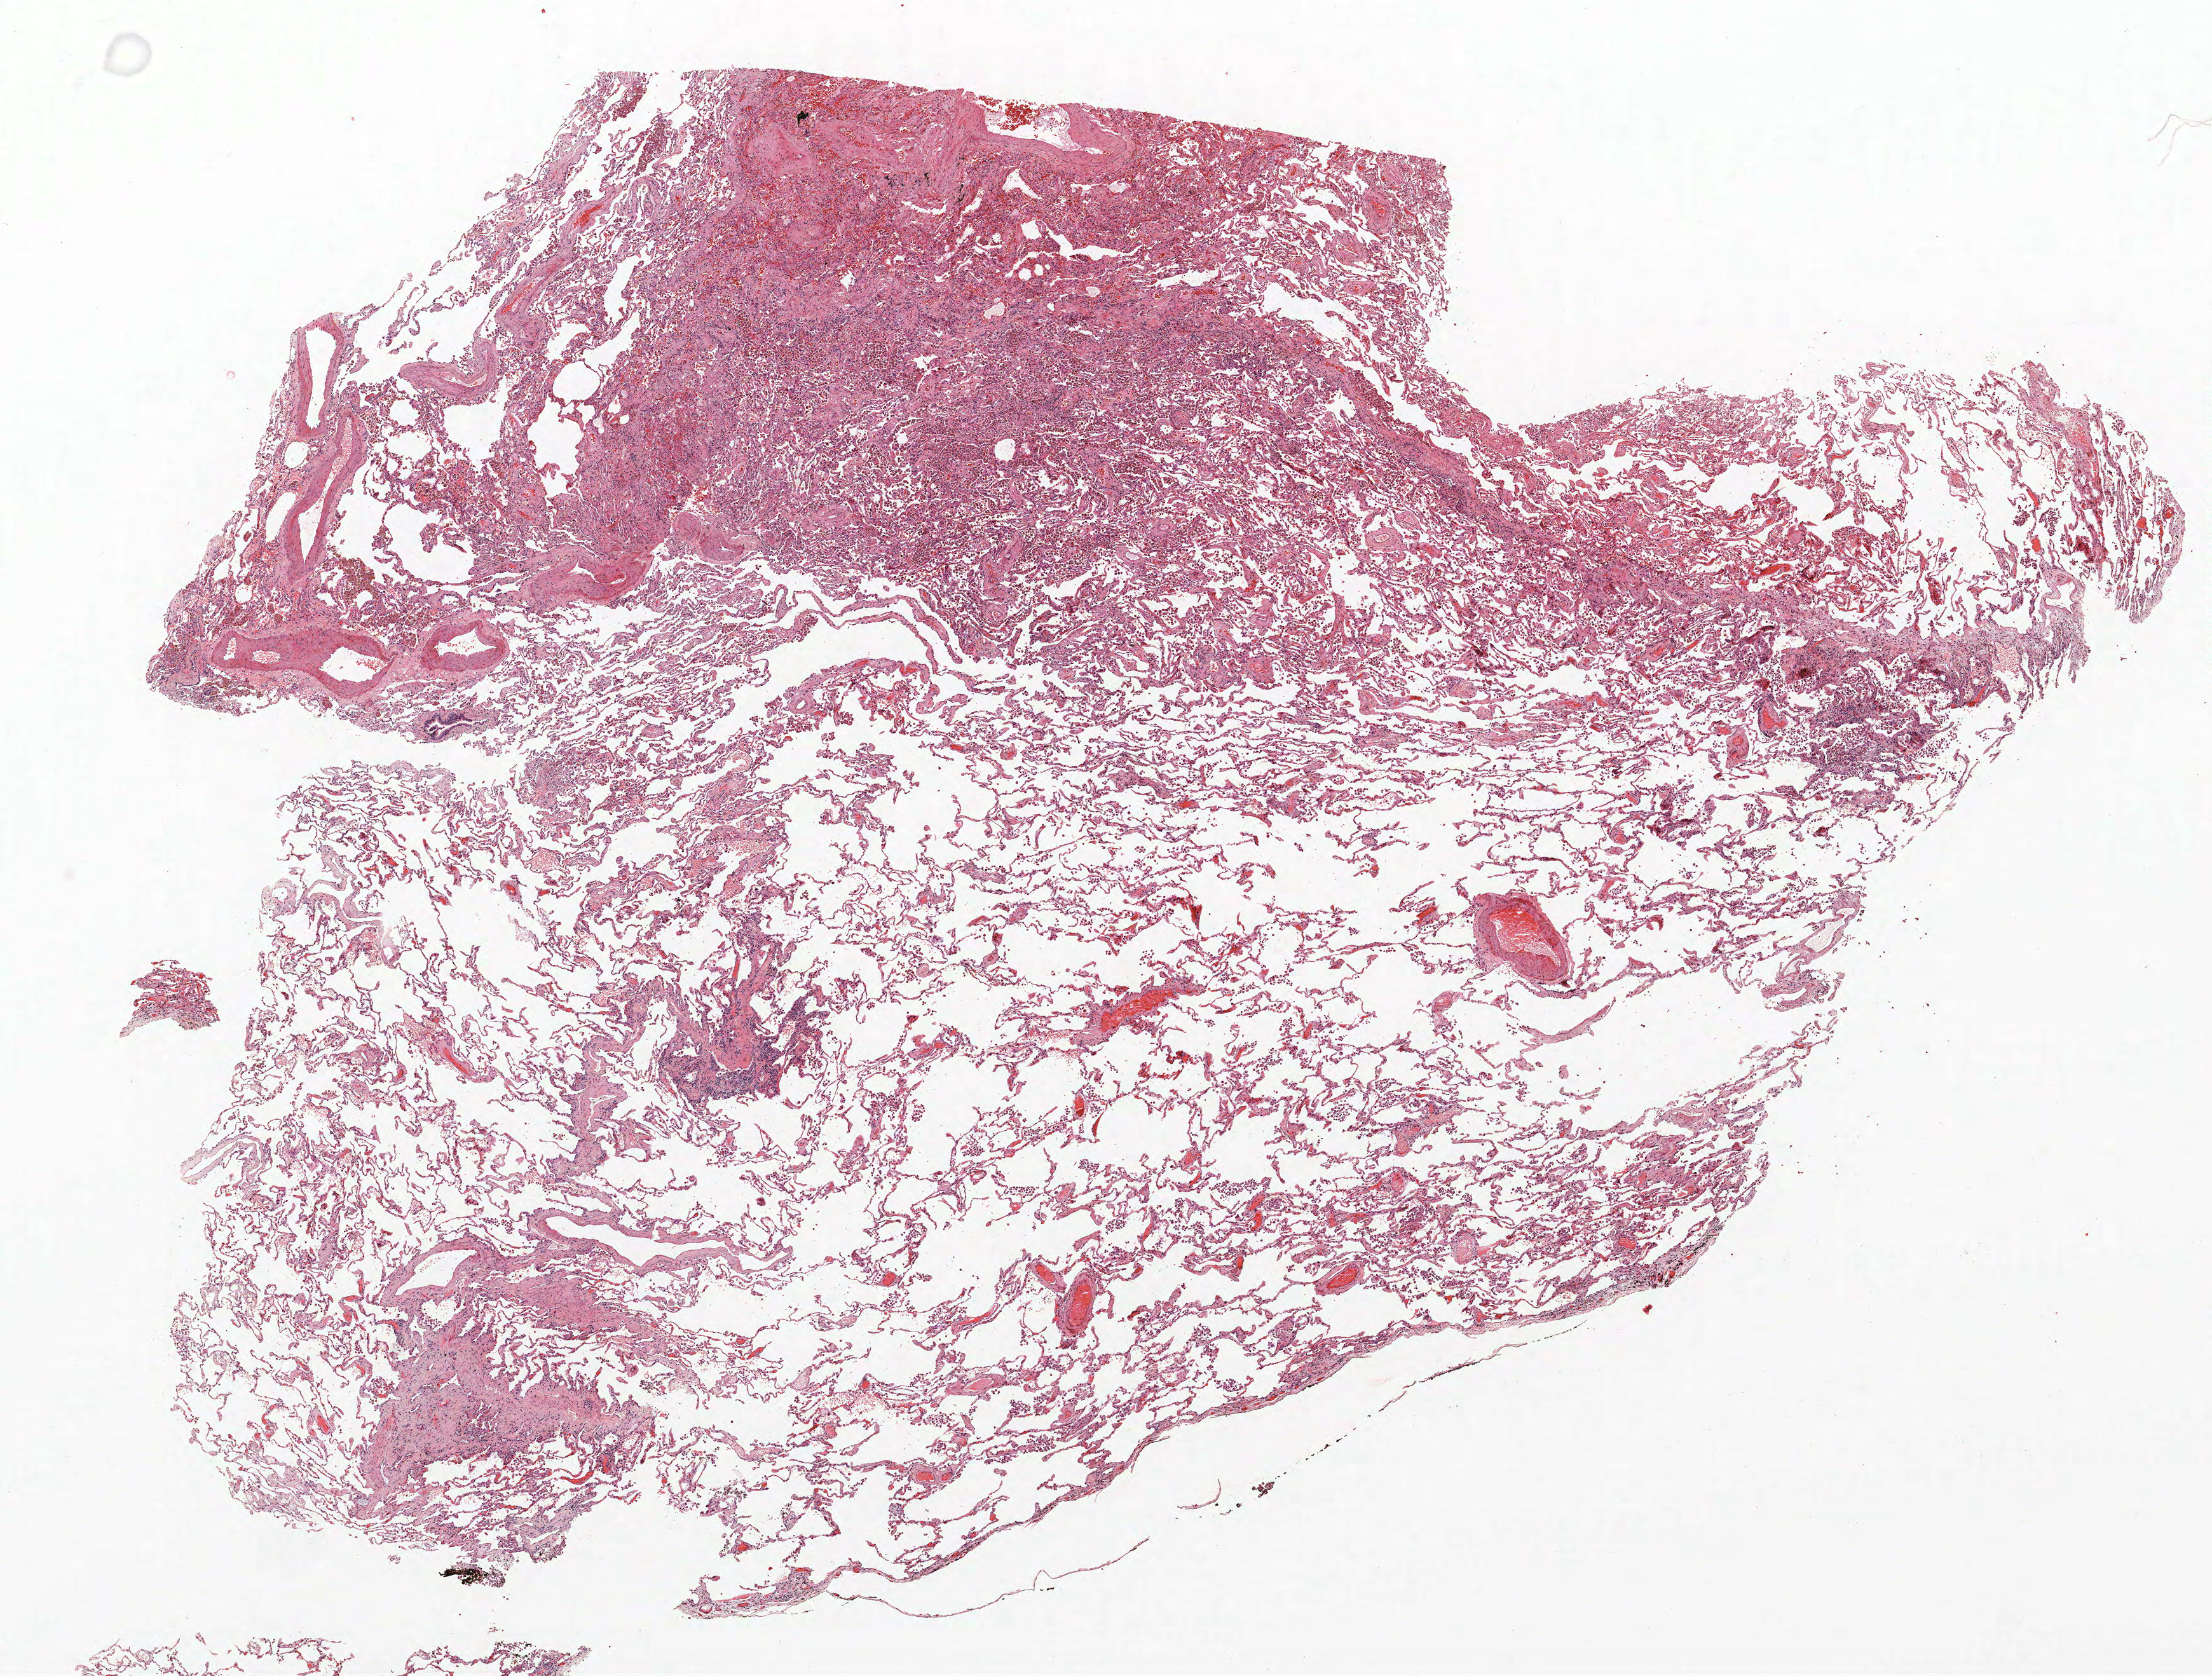
H&E whole-slide image — a low-resolution overview of the entire scanned area, about 13.9 x 10.5 mm (slide scanned at 40x). Formalin-fixed paraffin-embedded (FFPE) section. Lung. Male, age 73 at enrolment. Current smoker at enrolment. Grade: poorly differentiated (G3).
- primary tumour location (clinical record): right upper lobe
- stage (AJCC 6th edition): IIA
- tumour size (pathology): 30 mm
- participant's lung-cancer diagnosis: Adenocarcinoma, NOS